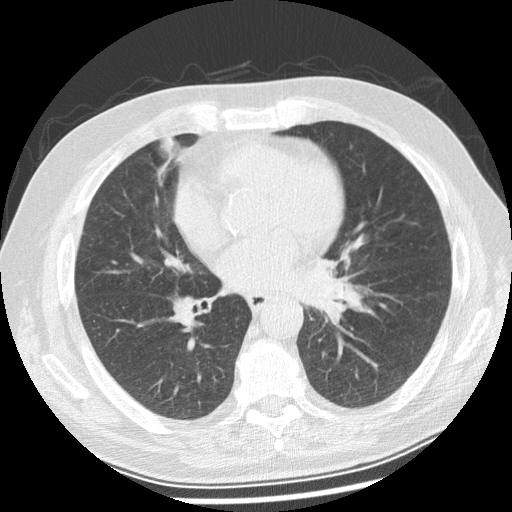
Low-dose screening chest CT, one axial slice. Position 123 of 250 along the scan axis. Reconstruction kernel STANDARD. Lung window (W 1500 / L -600 HU). 512 × 512 image matrix.
Annotated regions visible in this slice (manually delineated by an expert):
- lesion 1 (tumor, left main bronchus): bounding box <320,257,341,279> (left, top, right, bottom; pixels)